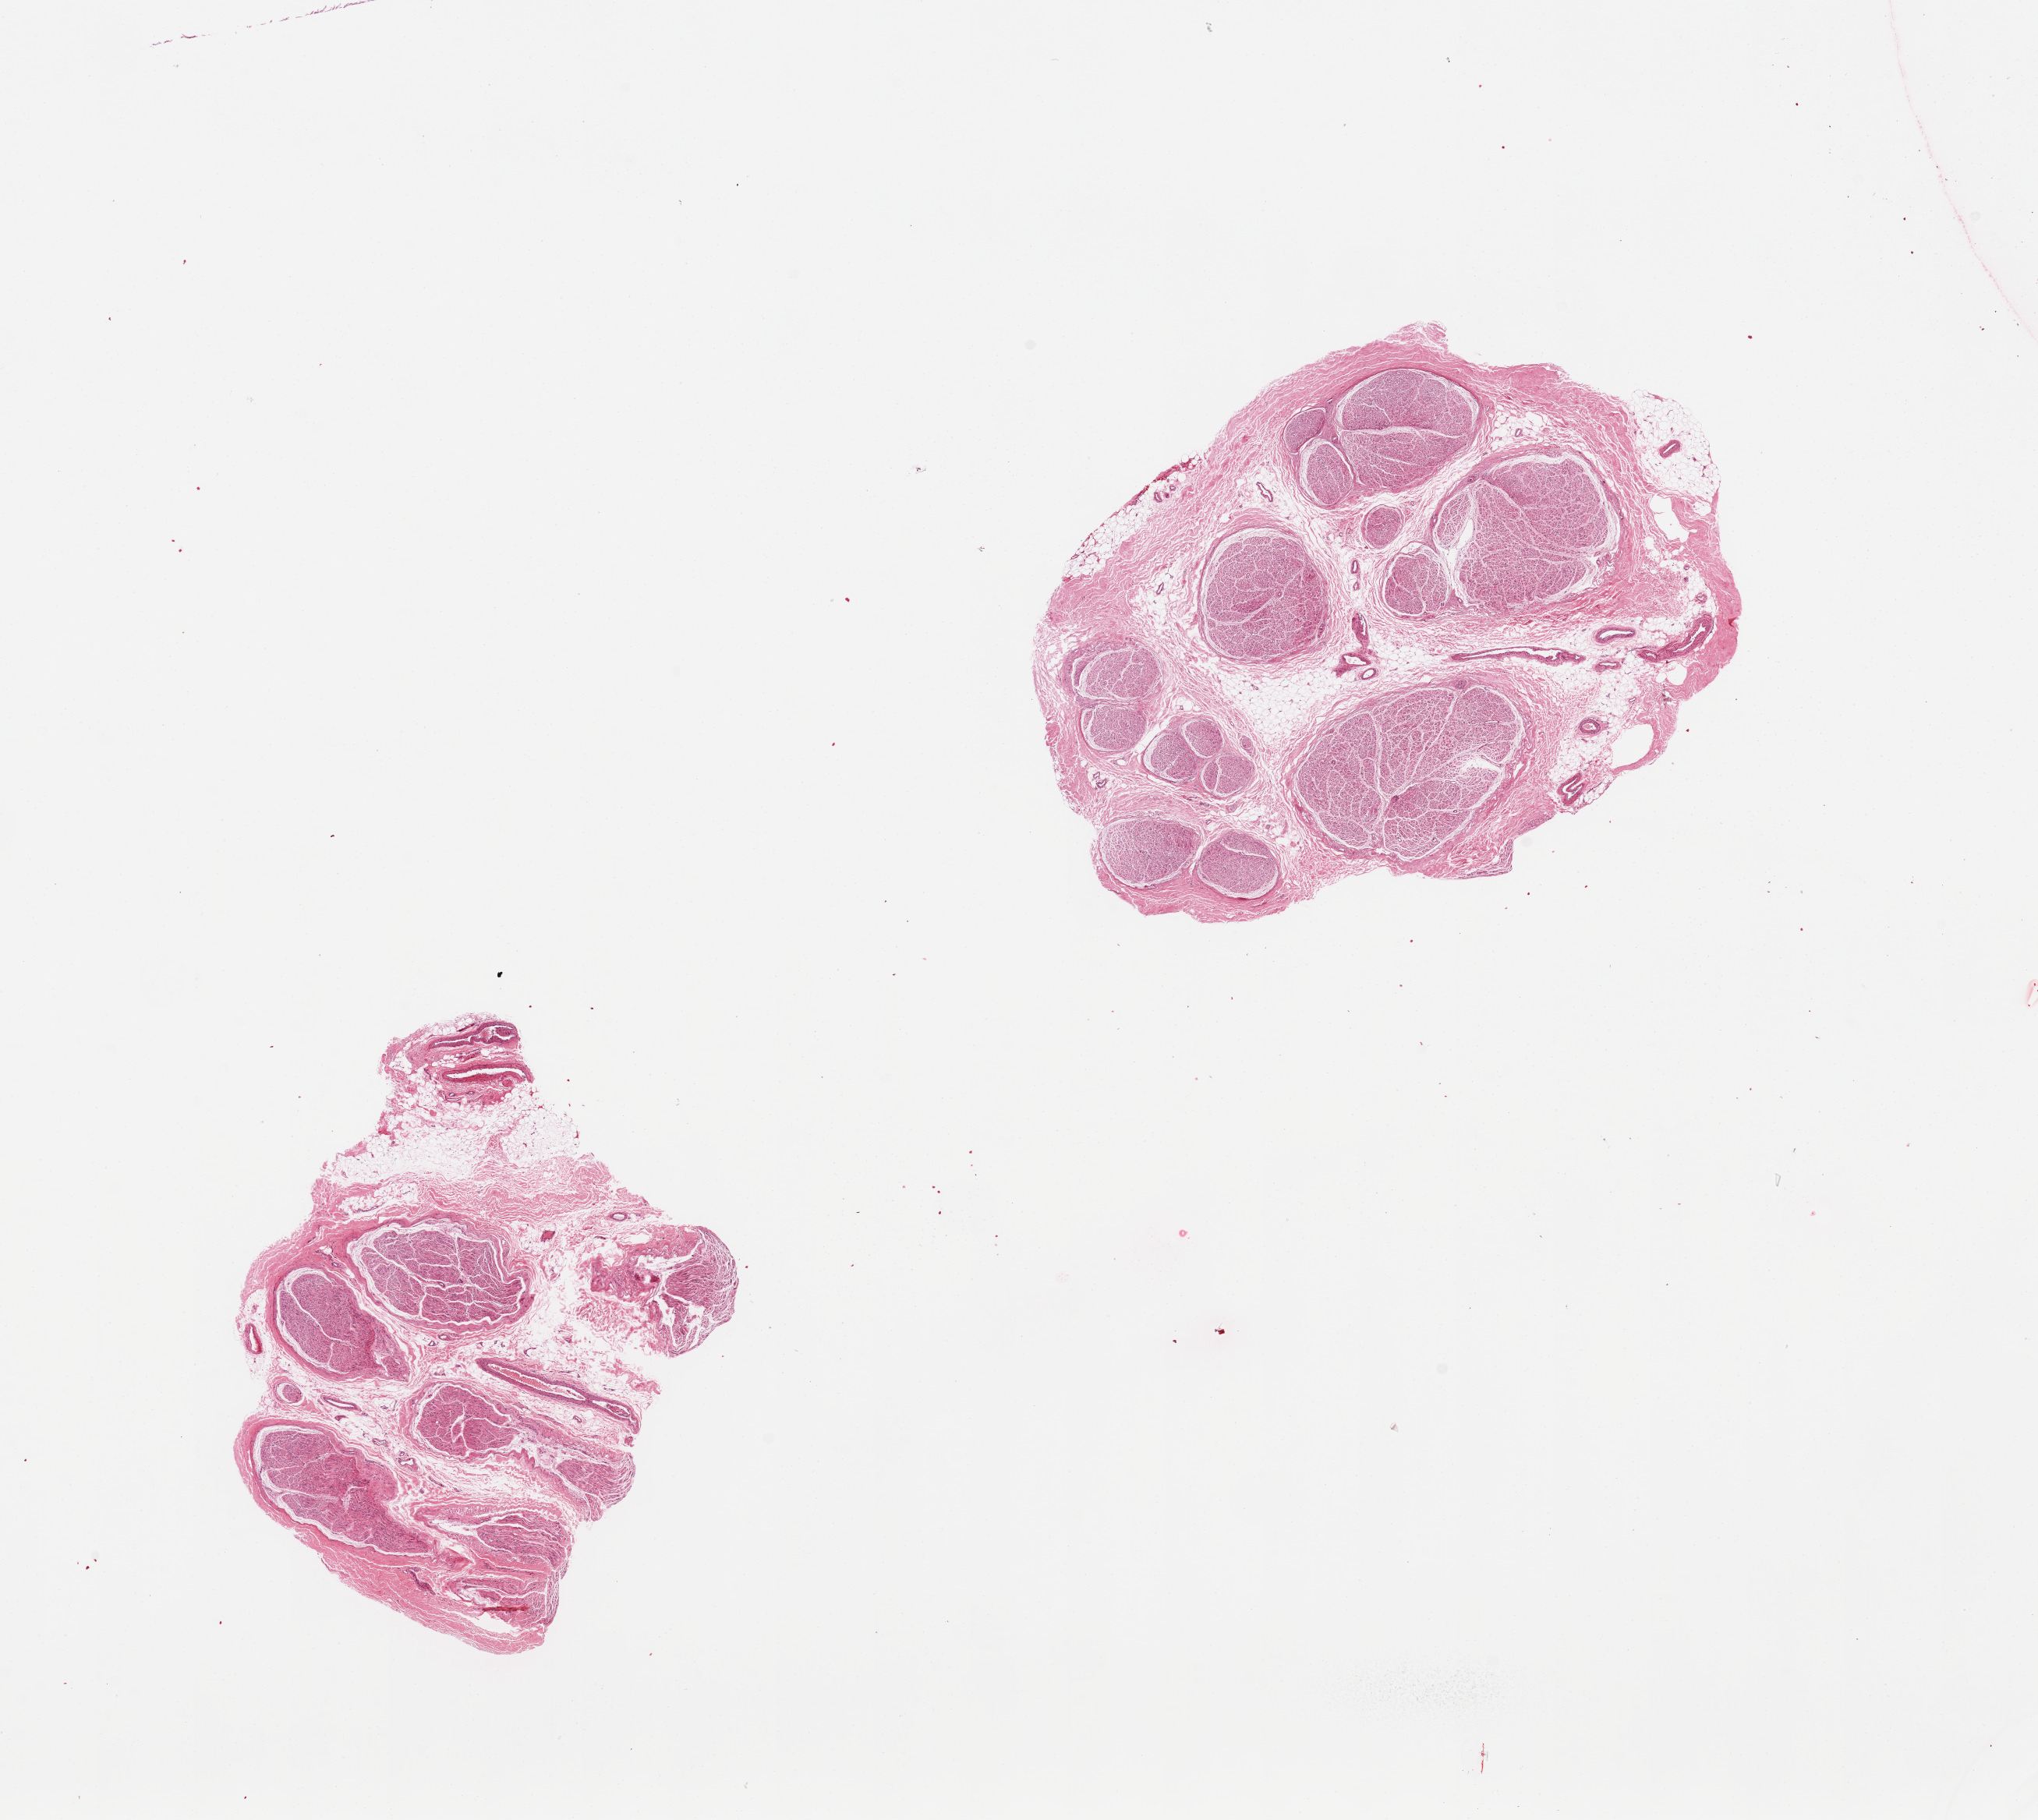
Whole-slide image, H&E stain, brightfield — whole scanned area (about 20.7 x 18.5 mm, from a 20x scan) shown as a low-resolution overview. PAXgene-fixed, paraffin-embedded tissue. Section of tibial nerve (target tissue). Tissue donor sample.
Reviewer comment on this tissue sample: 2 pieces, both include some attached fat and vascular tissue.